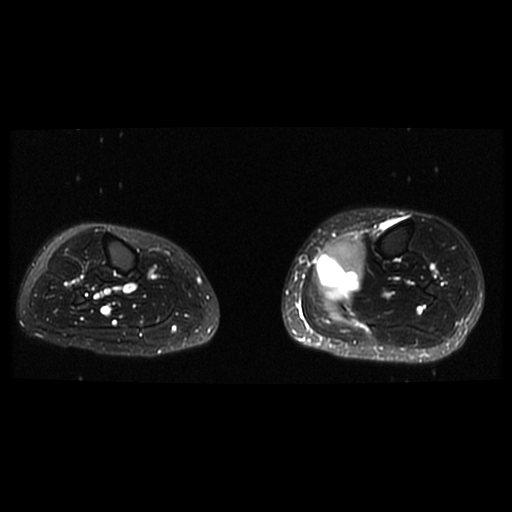
MRI of an extremity soft-tissue mass, one axial slice. Position 11 of 38 along the scan axis. T2-weighted fat-saturated. 6 mm slice thickness. 512 × 512 image matrix, field of view 330 × 330 mm. Female patient. From the clinical record (not read from this slice): histological type: extraskeletal high grade osteogenic sarcoma; grade: high; site of the primary tumour: left calf.
Structures marked on this image (manually delineated by an expert):
- gross tumour volume (mass): bounding box <314,238,365,301> (left, top, right, bottom; pixels)